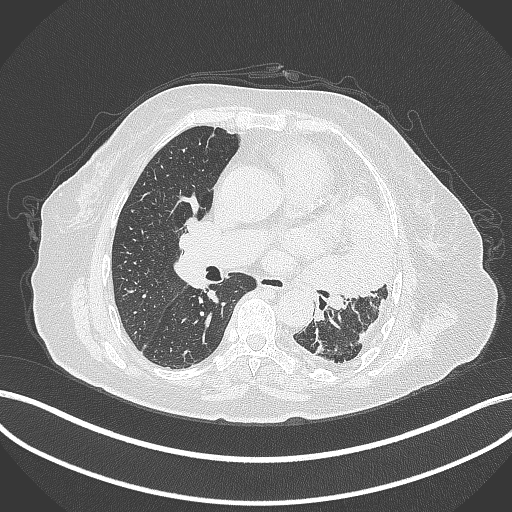
Chest CT, one axial slice; slice 196 of 399 in the series (ordered by position); reconstruction kernel B70f; lung window (W 1500 / L -600 HU); 1 mm slice thickness; 512 × 512 image matrix, field of view 400 × 400 mm. Female patient, age 75 years. Case-level facts recorded for this patient, not image findings: clinical TNM (as recorded): T3 N3 M1.
Structures marked on this image (bounding box drawn by a radiologist):
- lung tumour (recorded histology: adenocarcinoma): bounding box [x1, y1, x2, y2] px = [308, 189, 397, 312]